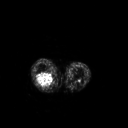
FDG PET of an extremity soft-tissue mass (from a PET/CT study), one axial slice. Slice 181 of 267 in the series (ordered by position). 3.27 mm slice thickness. 128 × 128 image matrix. Patient: female, 62 years. From the clinical record (not read from this slice): histological type: liposarcoma; site of the primary tumour: right thigh.
Structures marked on this image (expert contour drawn on MRI and transferred to this co-registered scan by the dataset authors):
- gross tumour volume (mass): bounding box <36,72,54,88> (left, top, right, bottom; pixels)